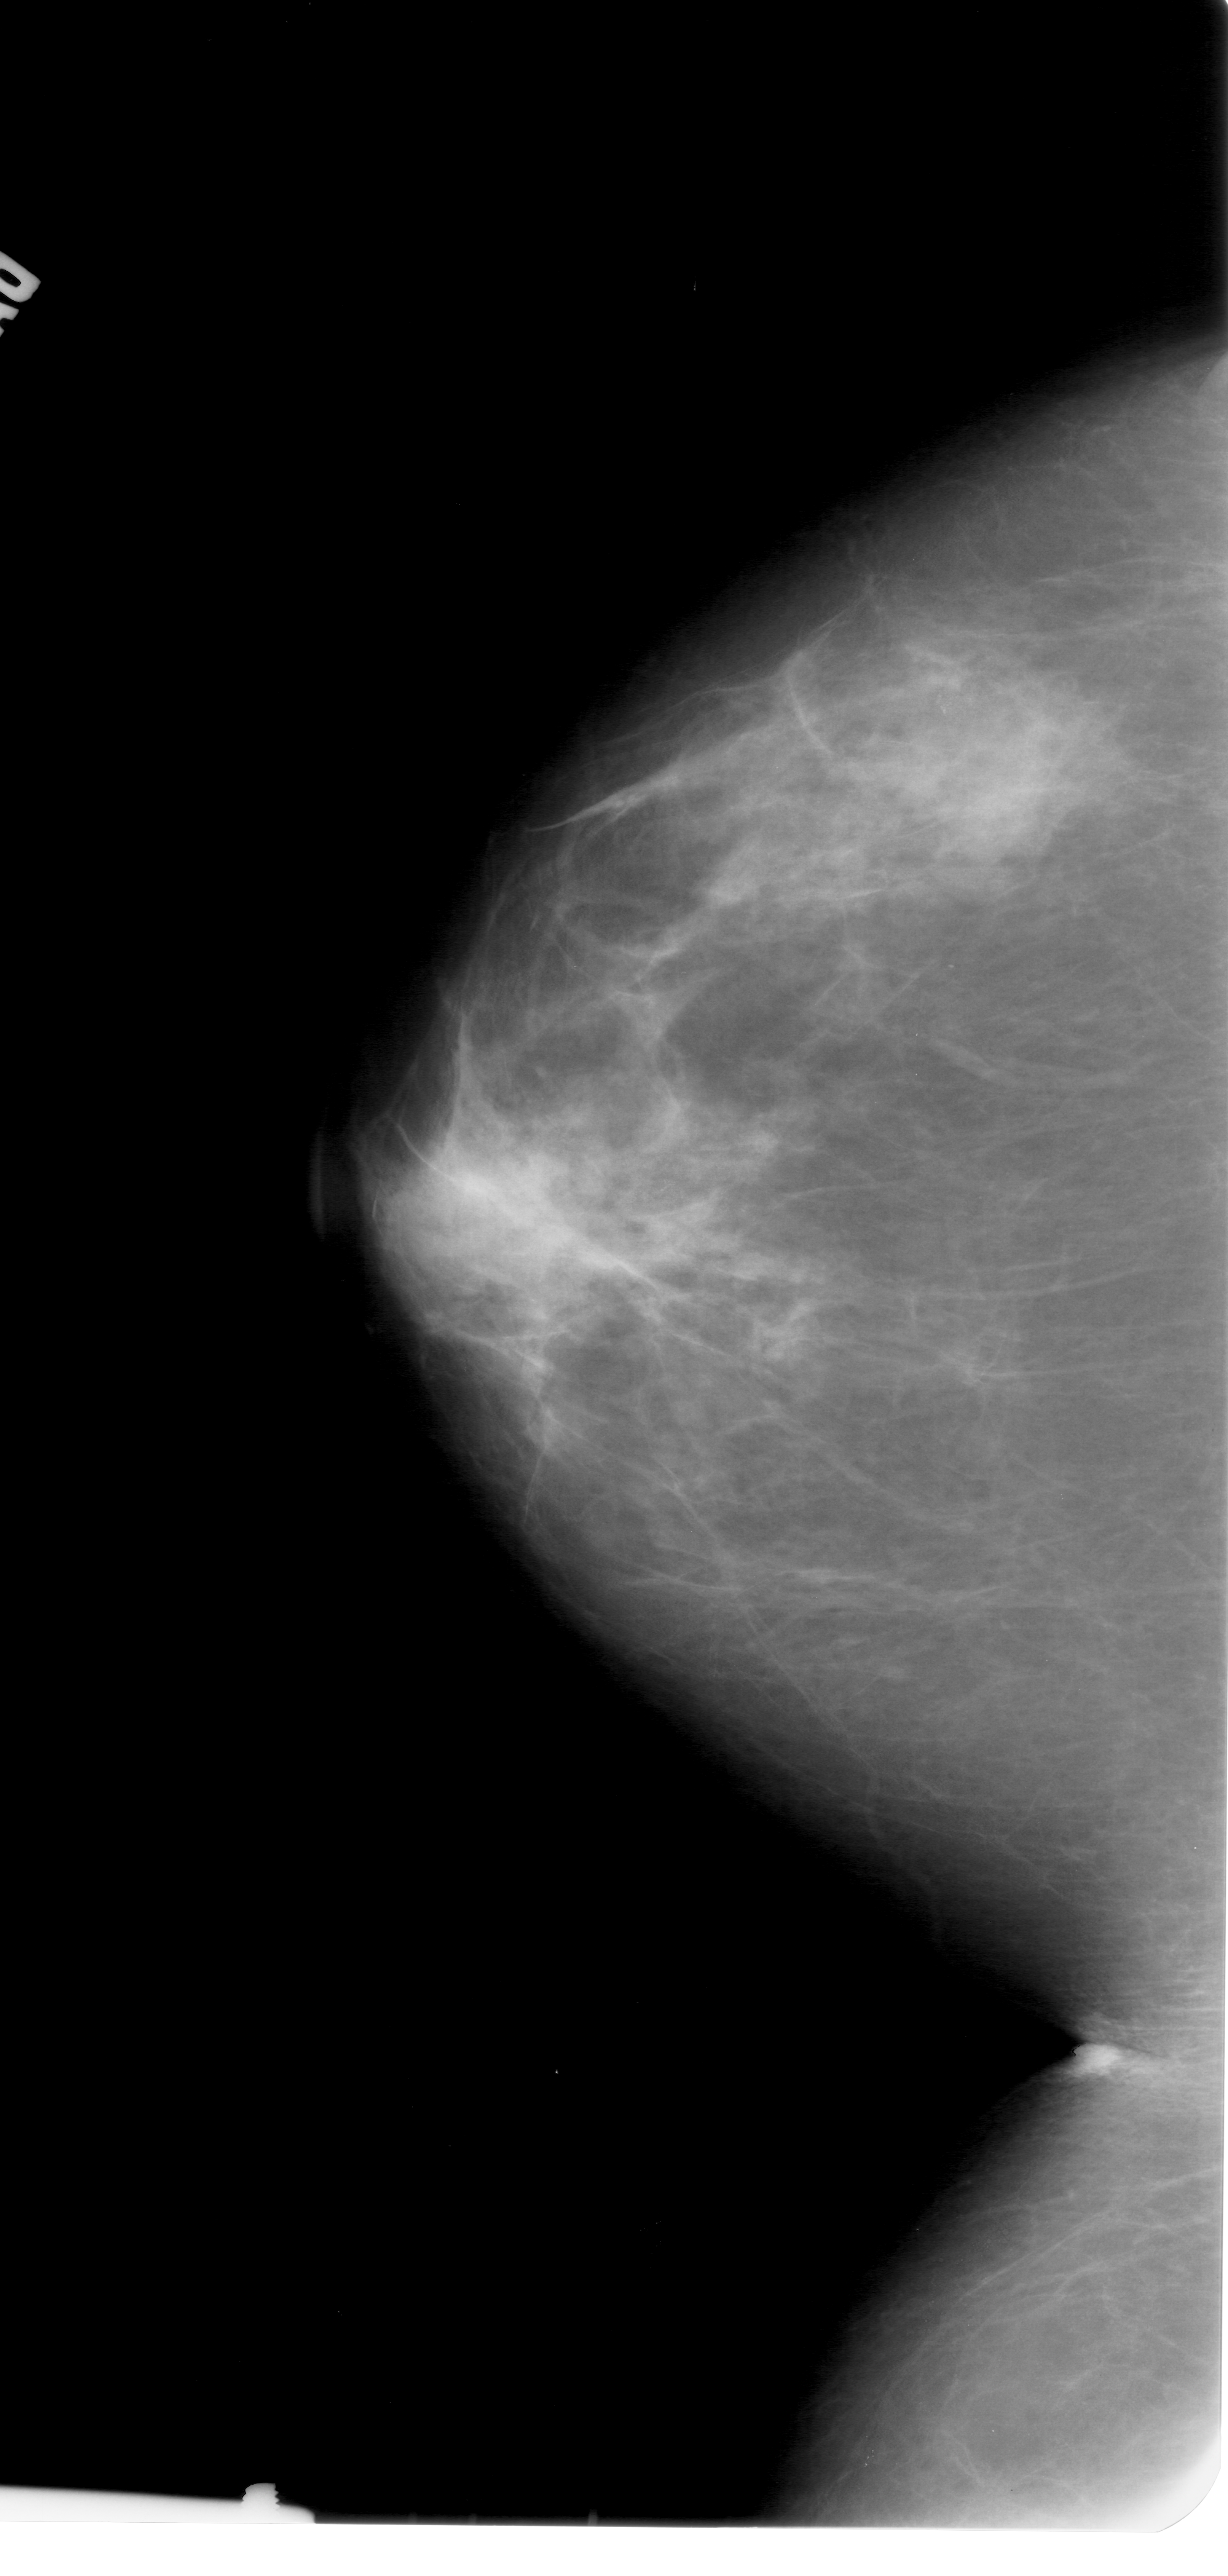
Scanned film-screen mammogram. Left breast. CC view. Breast composition: heterogeneously dense (BI-RADS density category 3 of 4). 1228 × 2576 image matrix.
Marked abnormalities (boxes around the expert regions of interest):
- calcifications, morphology pleomorphic, distribution clustered; BI-RADS assessment category 4; pathology (as recorded): malignant: bounding box <878,631,1028,773> (left, top, right, bottom; pixels)